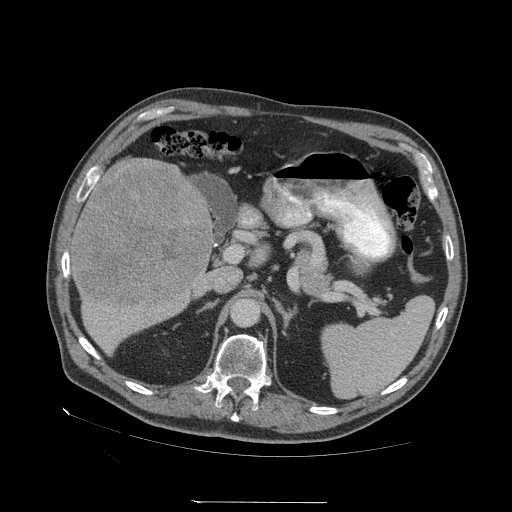
Contrast-enhanced abdominal CT (liver protocol), one axial slice; slice 27 of 83 in the series (ordered by position); reconstruction kernel STANDARD; soft-tissue window (W 400 / L 40 HU); 2.5 mm slice thickness; 512 × 512 image matrix, field of view 460 × 460 mm. Case-level facts recorded for this patient, not image findings: diagnosis: hepatocellular carcinoma (patient treated with transarterial chemoembolisation; whether this scan precedes or follows treatment is not stated here); TNM stage (as recorded): Stage-I; Child-Pugh class: A; tumour differentiation: well differentiated; tumour nodularity: uninodular.
Annotated regions visible in this slice (semi-automatically segmented with operator editing):
- liver parenchyma outside the tumour (the mass and vessels are separate outlines, so this box may not span the whole liver): bounding box <70,158,214,354> (left, top, right, bottom; pixels)
- mass: <72,158,211,304>